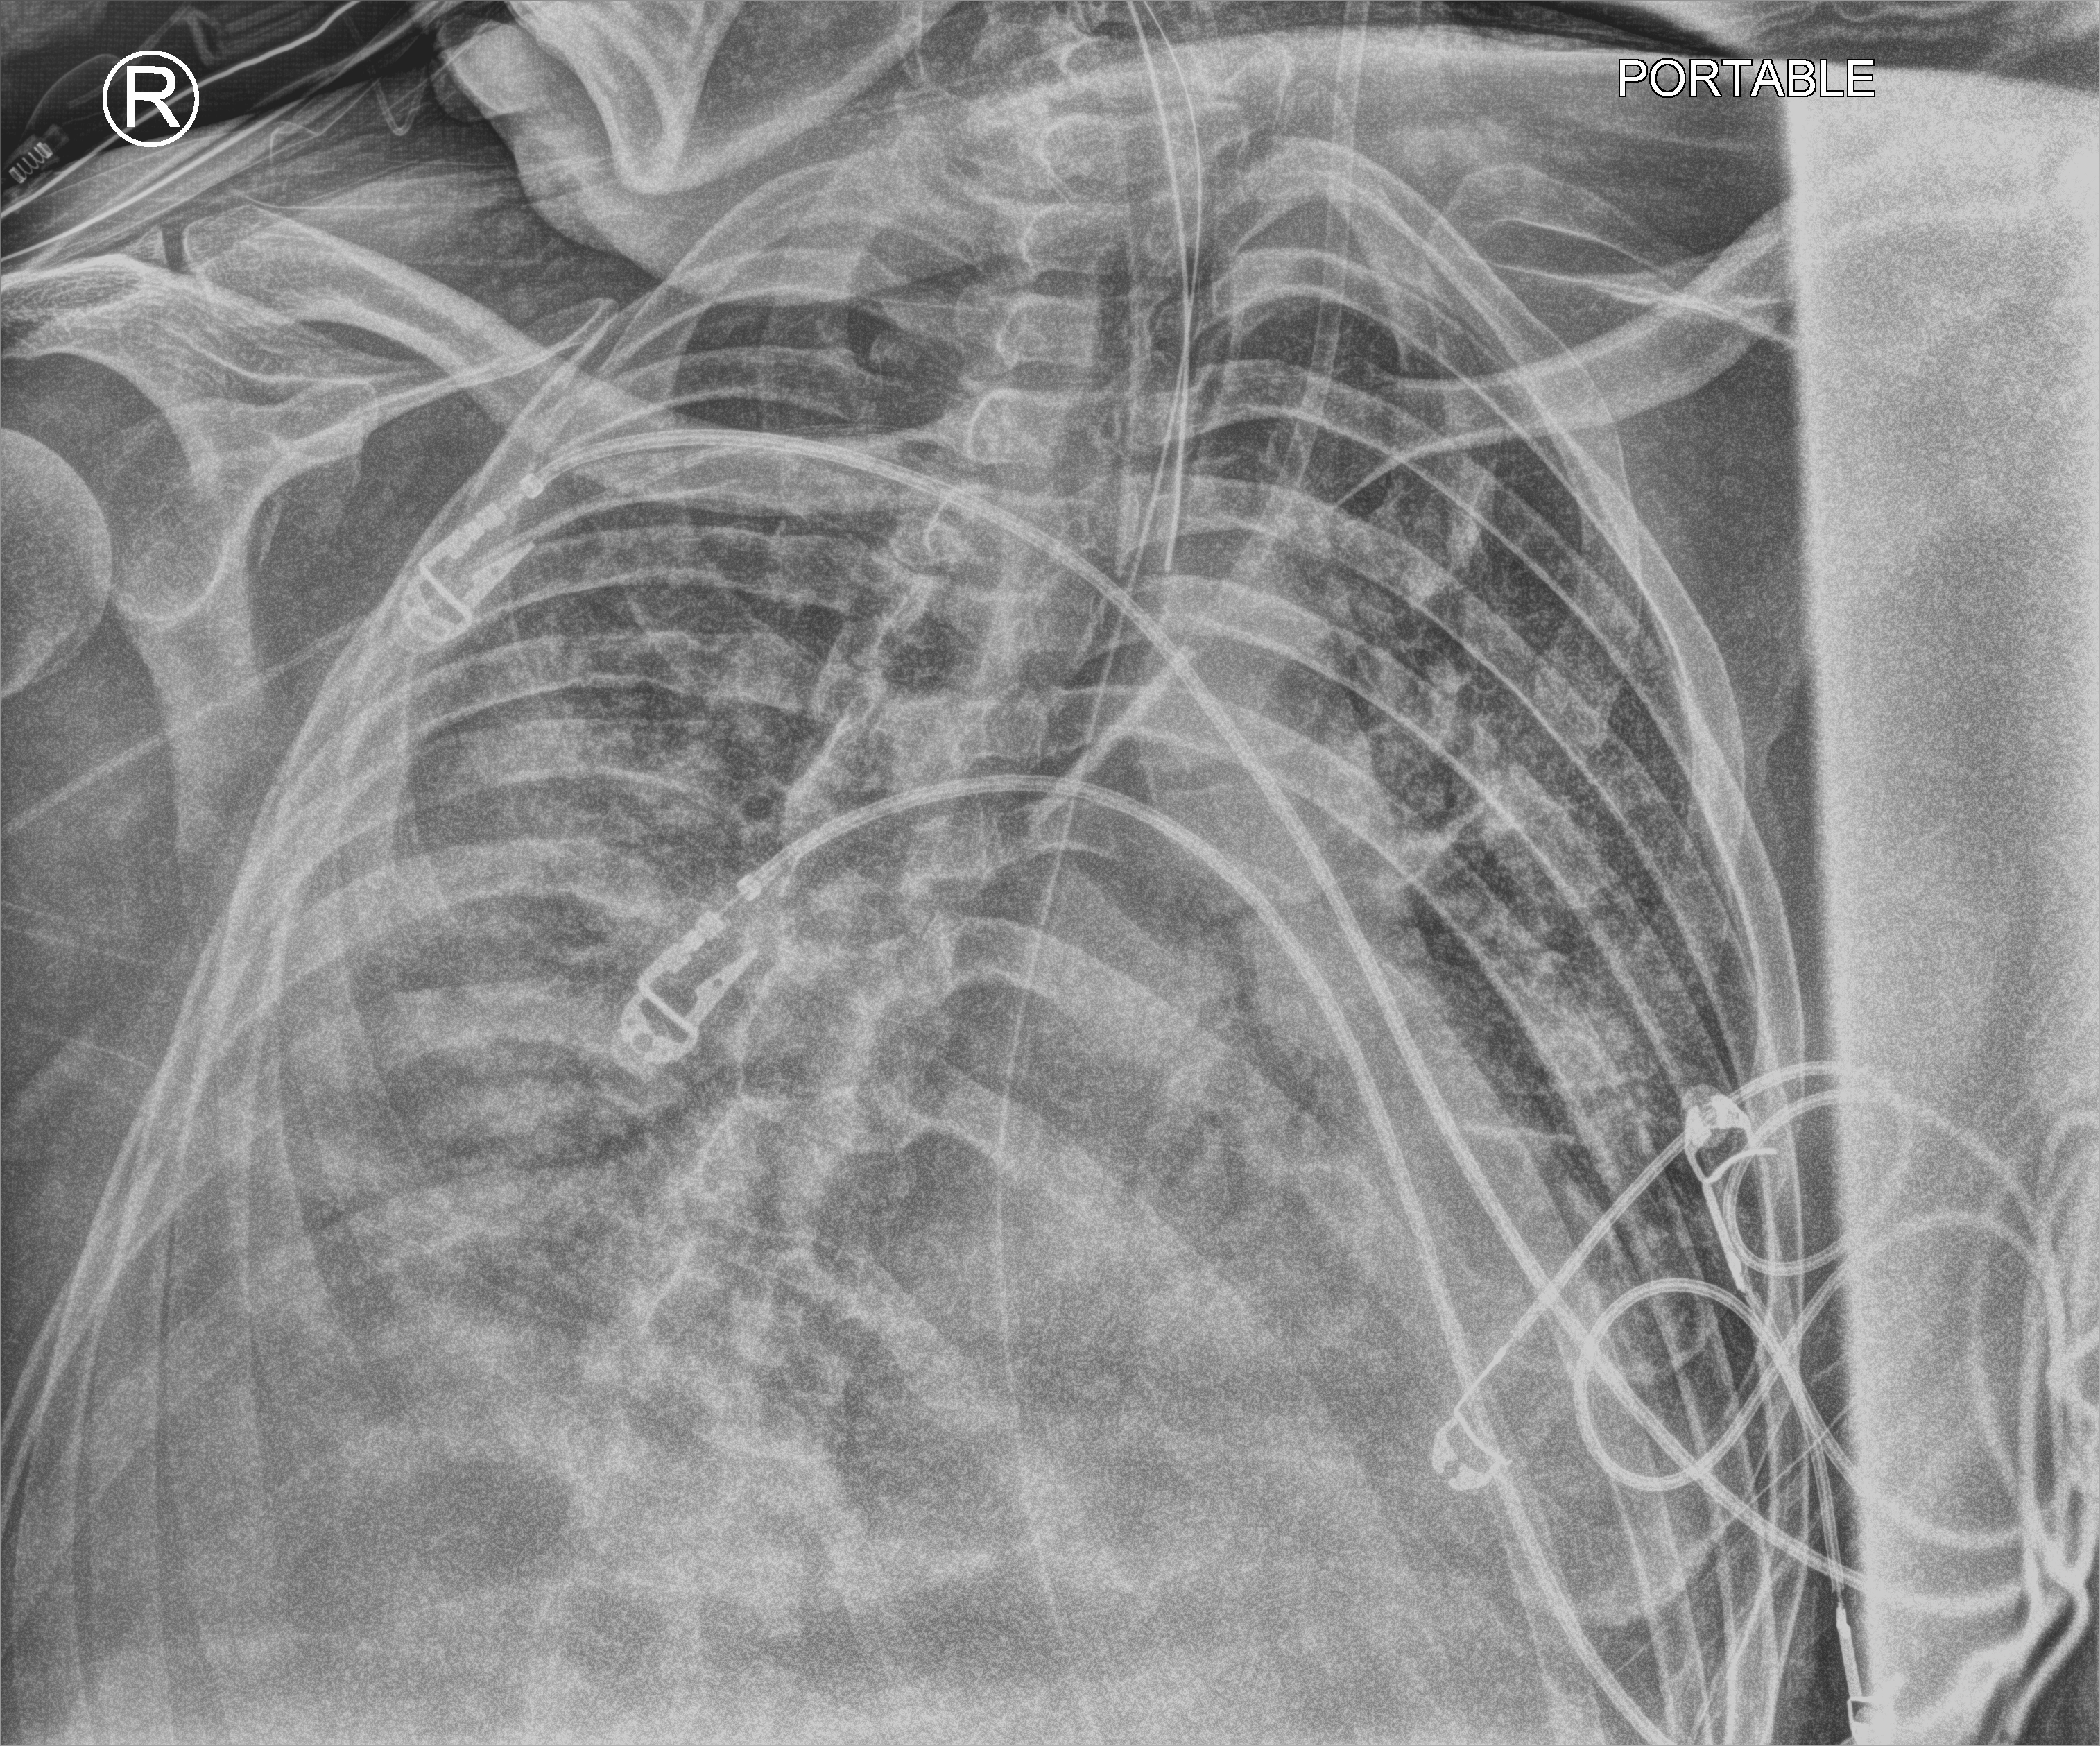
Bedside chest radiograph (computed radiography); anteroposterior (AP) projection. Male patient hospitalised with COVID-19, age 18–59 years.
From the hospital-stay record, not from the radiograph (when in the stay this image was taken is not recorded):
- admitted to intensive care during this hospital stay: yes
- diabetes (admission record): no